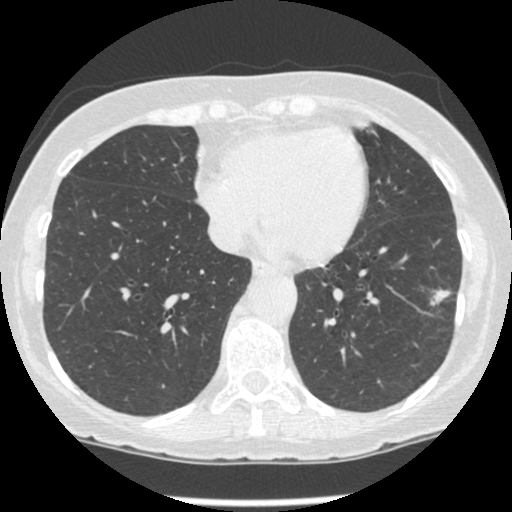
Low-dose screening chest CT, one axial slice; reconstruction kernel STANDARD; 120 kVp; lung window (W 1500 / L -600 HU); 1.25 mm slice thickness; 512 × 512 image matrix, field of view 303 × 303 mm.
Annotated regions visible in this slice (outlined manually by an expert reader):
- lesion 1 (tumor, lower lobe of left lung): bounding box [x1, y1, x2, y2] px = [431, 289, 451, 305]